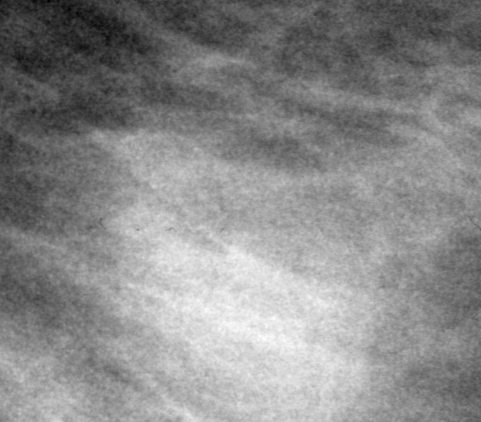
Region of interest cut from a scanned film mammogram (one marked finding), left breast, MLO view.
Finding: mass, shape oval, margins microlobulated; BI-RADS assessment category 0 (incomplete: needs additional imaging); subtlety rating 5 on a 1 (subtle) to 5 (obvious) scale; pathology result (as recorded, not read from the image): benign.